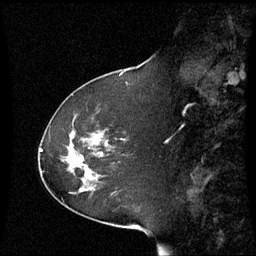
Breast MRI (dynamic contrast-enhanced), one sagittal slice; position 23 of 60 along the scan axis; dynamic contrast-enhanced series, image 2 of 3 at this slice position (ordered by acquisition); 1.5 T; TE 4.2 ms, TR 8.9 ms; 2.4 mm slice thickness; 256 × 256 image matrix, field of view 230 × 230 mm. Female patient, age 51 years. From the clinical record (not read from this slice): setting: breast cancer imaged before/during neoadjuvant chemotherapy; receptor status: HR-positive, HER2-negative.
Outlined on this slice (semi-automatically segmented with operator editing):
- analysis volume of interest (the breast-tissue region the enhancement analysis was run in; not a lesion): bounding box [x1, y1, x2, y2] px = [42, 121, 109, 194]
- tumour enhancement mask (voxels above the 70 % enhancement threshold inside the analysis volume of interest): [68, 155, 81, 166]